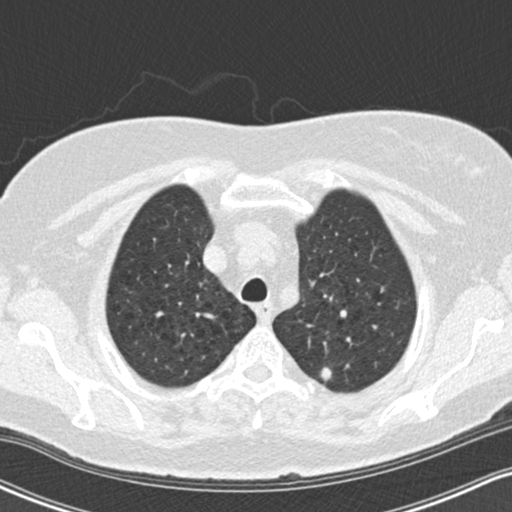
Low-dose screening chest CT, one axial slice; reconstruction kernel B30f; 120 kVp; lung window (W 1500 / L -600 HU); 2 mm slice thickness; 512 × 512 image matrix.
Structures marked on this image (outlined manually by an expert reader):
- lesion 1 (tumor, upper lobe of left lung): box from (x=320, y=367) to (x=333, y=381) px